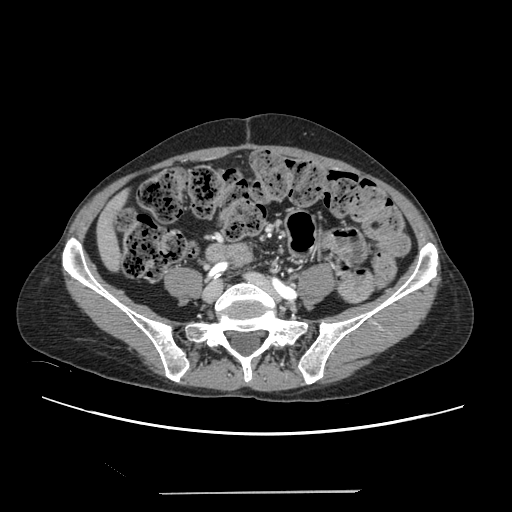
Contrast-enhanced abdominal CT, one axial slice; slice 14 of 240 in the series (ordered by position); 120 kVp; intravenous contrast given; soft-tissue window (W 400 / L 40 HU); 512 × 512 image matrix, field of view 371 × 371 mm. Female patient, age 60 years. Case-level facts recorded for this patient, not image findings: diagnosis: colorectal cancer liver metastases, imaged before liver resection; multiple liver metastases: no; largest metastasis: 1.5 cm; disease in both lobes: no.
Annotated regions visible in this slice (expert manual segmentation):
- liver: bounding box <99,204,119,268> (left, top, right, bottom; pixels)
- planned liver remnant (the part of the liver to remain after resection): <99,203,119,268>